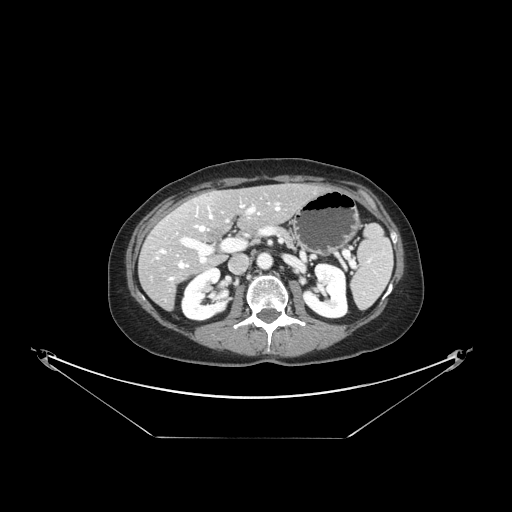
Contrast-enhanced abdominal CT, one axial slice. Reconstruction kernel STANDARD. Soft-tissue window (W 400 / L 40 HU). 2.5 mm slice thickness. 512 × 512 image matrix. Female patient, age 73 years. From the clinical record (not read from this slice): diagnosis: colorectal cancer liver metastases, imaged before liver resection; multiple liver metastases: no; largest metastasis: 1 cm; disease in both lobes: no.
Annotated regions visible in this slice (manually delineated by an expert):
- hepatic veins: bounding box (x1, y1, x2, y2) in pixels: (157, 204, 280, 280)
- liver: (141, 184, 320, 308)
- planned liver remnant (the part of the liver to remain after resection): (168, 184, 321, 241)
- portal vein (with intrahepatic branches): (176, 205, 260, 263)